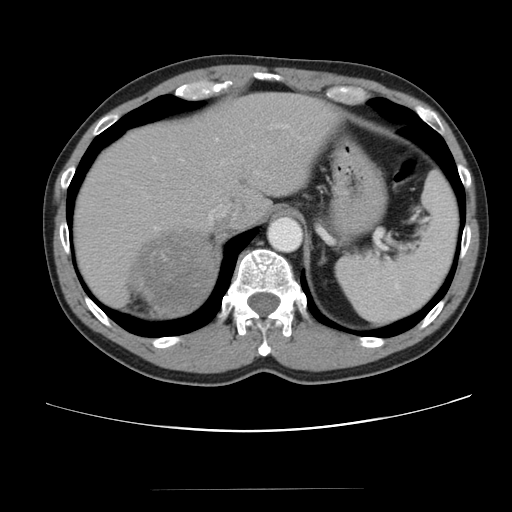
Contrast-enhanced abdominal CT, one axial slice; position 70 of 80 along the scan axis; reconstruction kernel STANDARD; 120 kVp; intravenous contrast given; soft-tissue window (W 400 / L 40 HU); 512 × 512 image matrix, field of view 360 × 360 mm. Patient: male, 61 years. Case-level facts recorded for this patient, not image findings: diagnosis: adrenocortical carcinoma; tumour side: right adrenal; tumour size at pathology: 11.1 cm.
Outlined on this slice (semi-automatically segmented with operator editing):
- mass: bounding box (x1, y1, x2, y2) in pixels: (131, 232, 216, 317)